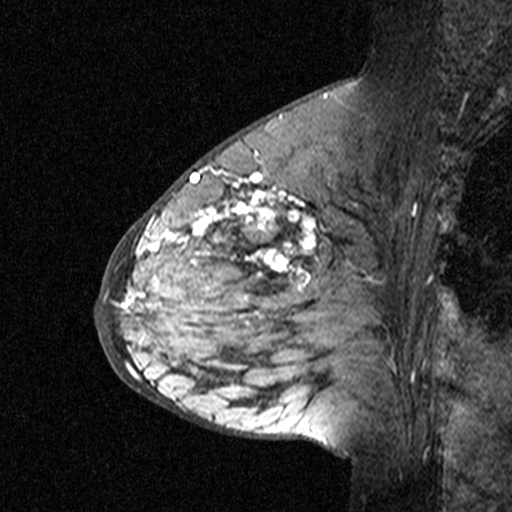
Breast MRI (dynamic contrast-enhanced), one sagittal slice. Slice 18 of 44 in the series (ordered by position). Dynamic contrast-enhanced study with each time point stored as its own series, time point 3 of 4 at this slice position (ordered by acquisition time). 1.5 T. TE 4.5 ms, TR 11 ms. 512 × 512 image matrix, field of view 200 × 200 mm. Female patient, age 65 years. From the clinical record (not read from this slice): setting: breast cancer imaged before/during neoadjuvant chemotherapy; receptor status: HER2-positive.
Outlined on this slice (semi-automatic segmentation, software-assisted and operator-edited):
- analysis volume of interest (the breast-tissue region the enhancement analysis was run in; not a lesion): bounding box [x1, y1, x2, y2] px = [182, 190, 353, 361]
- tumour enhancement mask (voxels above the 90 % enhancement threshold inside the analysis volume of interest): [182, 190, 316, 289]